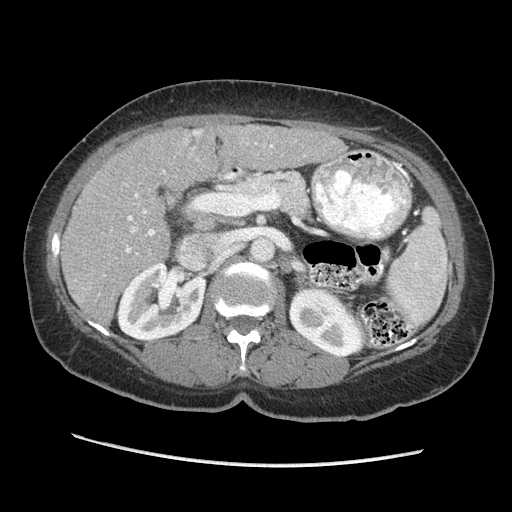
Contrast-enhanced abdominal CT (liver protocol), one axial slice; position 121 of 170 along the scan axis; reconstruction kernel STANDARD; soft-tissue window (W 400 / L 40 HU); 2.5 mm slice thickness; 512 × 512 image matrix, field of view 360 × 360 mm. From the clinical record (not read from this slice): diagnosis: hepatocellular carcinoma (patient treated with transarterial chemoembolisation; whether this scan precedes or follows treatment is not stated here); TNM stage (as recorded): Stage-II; Child-Pugh class: A; tumour differentiation: no biopsy; tumour nodularity: multinodular.
Annotated regions visible in this slice (semi-automatically segmented with operator editing):
- liver parenchyma outside the tumour (the mass and vessels are separate outlines, so this box may not span the whole liver): bounding box (x1, y1, x2, y2) in pixels: (62, 122, 346, 320)
- mass: (181, 126, 206, 152)
- liver vessels: (126, 143, 273, 253)